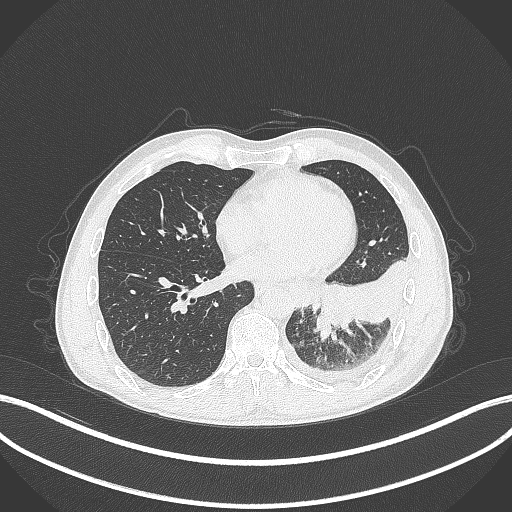
Chest CT, one axial slice; position 113 of 295 along the scan axis; reconstruction kernel B70f; 120 kVp; lung window (W 1500 / L -600 HU); 512 × 512 image matrix, field of view 400 × 400 mm. Male patient, age 47 years. Case-level facts recorded for this patient, not image findings: clinical TNM (as recorded): T3 N1 M1c; histopathological grade: G3.
Annotated regions visible in this slice (rectangle marked by the reading radiologist):
- lung tumour (recorded histology: small cell carcinoma): box from (x=311, y=311) to (x=332, y=342) px